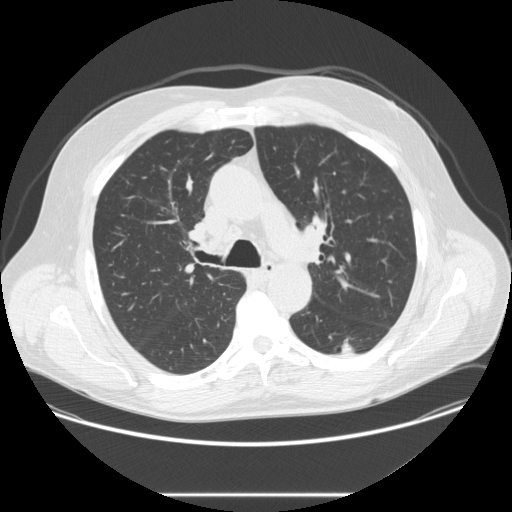
Low-dose screening chest CT, one axial slice. Position 173 of 262 along the scan axis. Reconstruction kernel STANDARD. Lung window (W 1500 / L -600 HU). 2.5 mm slice thickness. 512 × 512 image matrix, field of view 420 × 420 mm.
Structures marked on this image (manually delineated by an expert):
- lesion 1 (tumor, lower lobe of left lung): bounding box (x1, y1, x2, y2) in pixels: (340, 341, 355, 355)